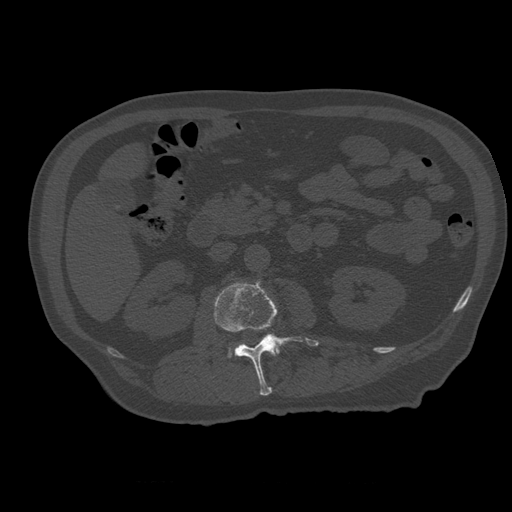
CT including the spine, one axial slice; slice 211 of 399 in the series (ordered by position); reconstruction kernel STANDARD; bone window (W 1800 / L 400 HU); 512 × 512 image matrix. Patient age 73 years. Case-level facts recorded for this patient, not image findings: primary cancer: prostate; vertebrae with lytic lesions (as recorded): L2.
Structures marked on this image (semi-automatically segmented with operator editing):
- L1 vertebra: bounding box [x1, y1, x2, y2] px = [267, 346, 281, 352]
- L2 vertebra: [214, 282, 303, 396]
- L3 vertebra: [228, 346, 280, 358]